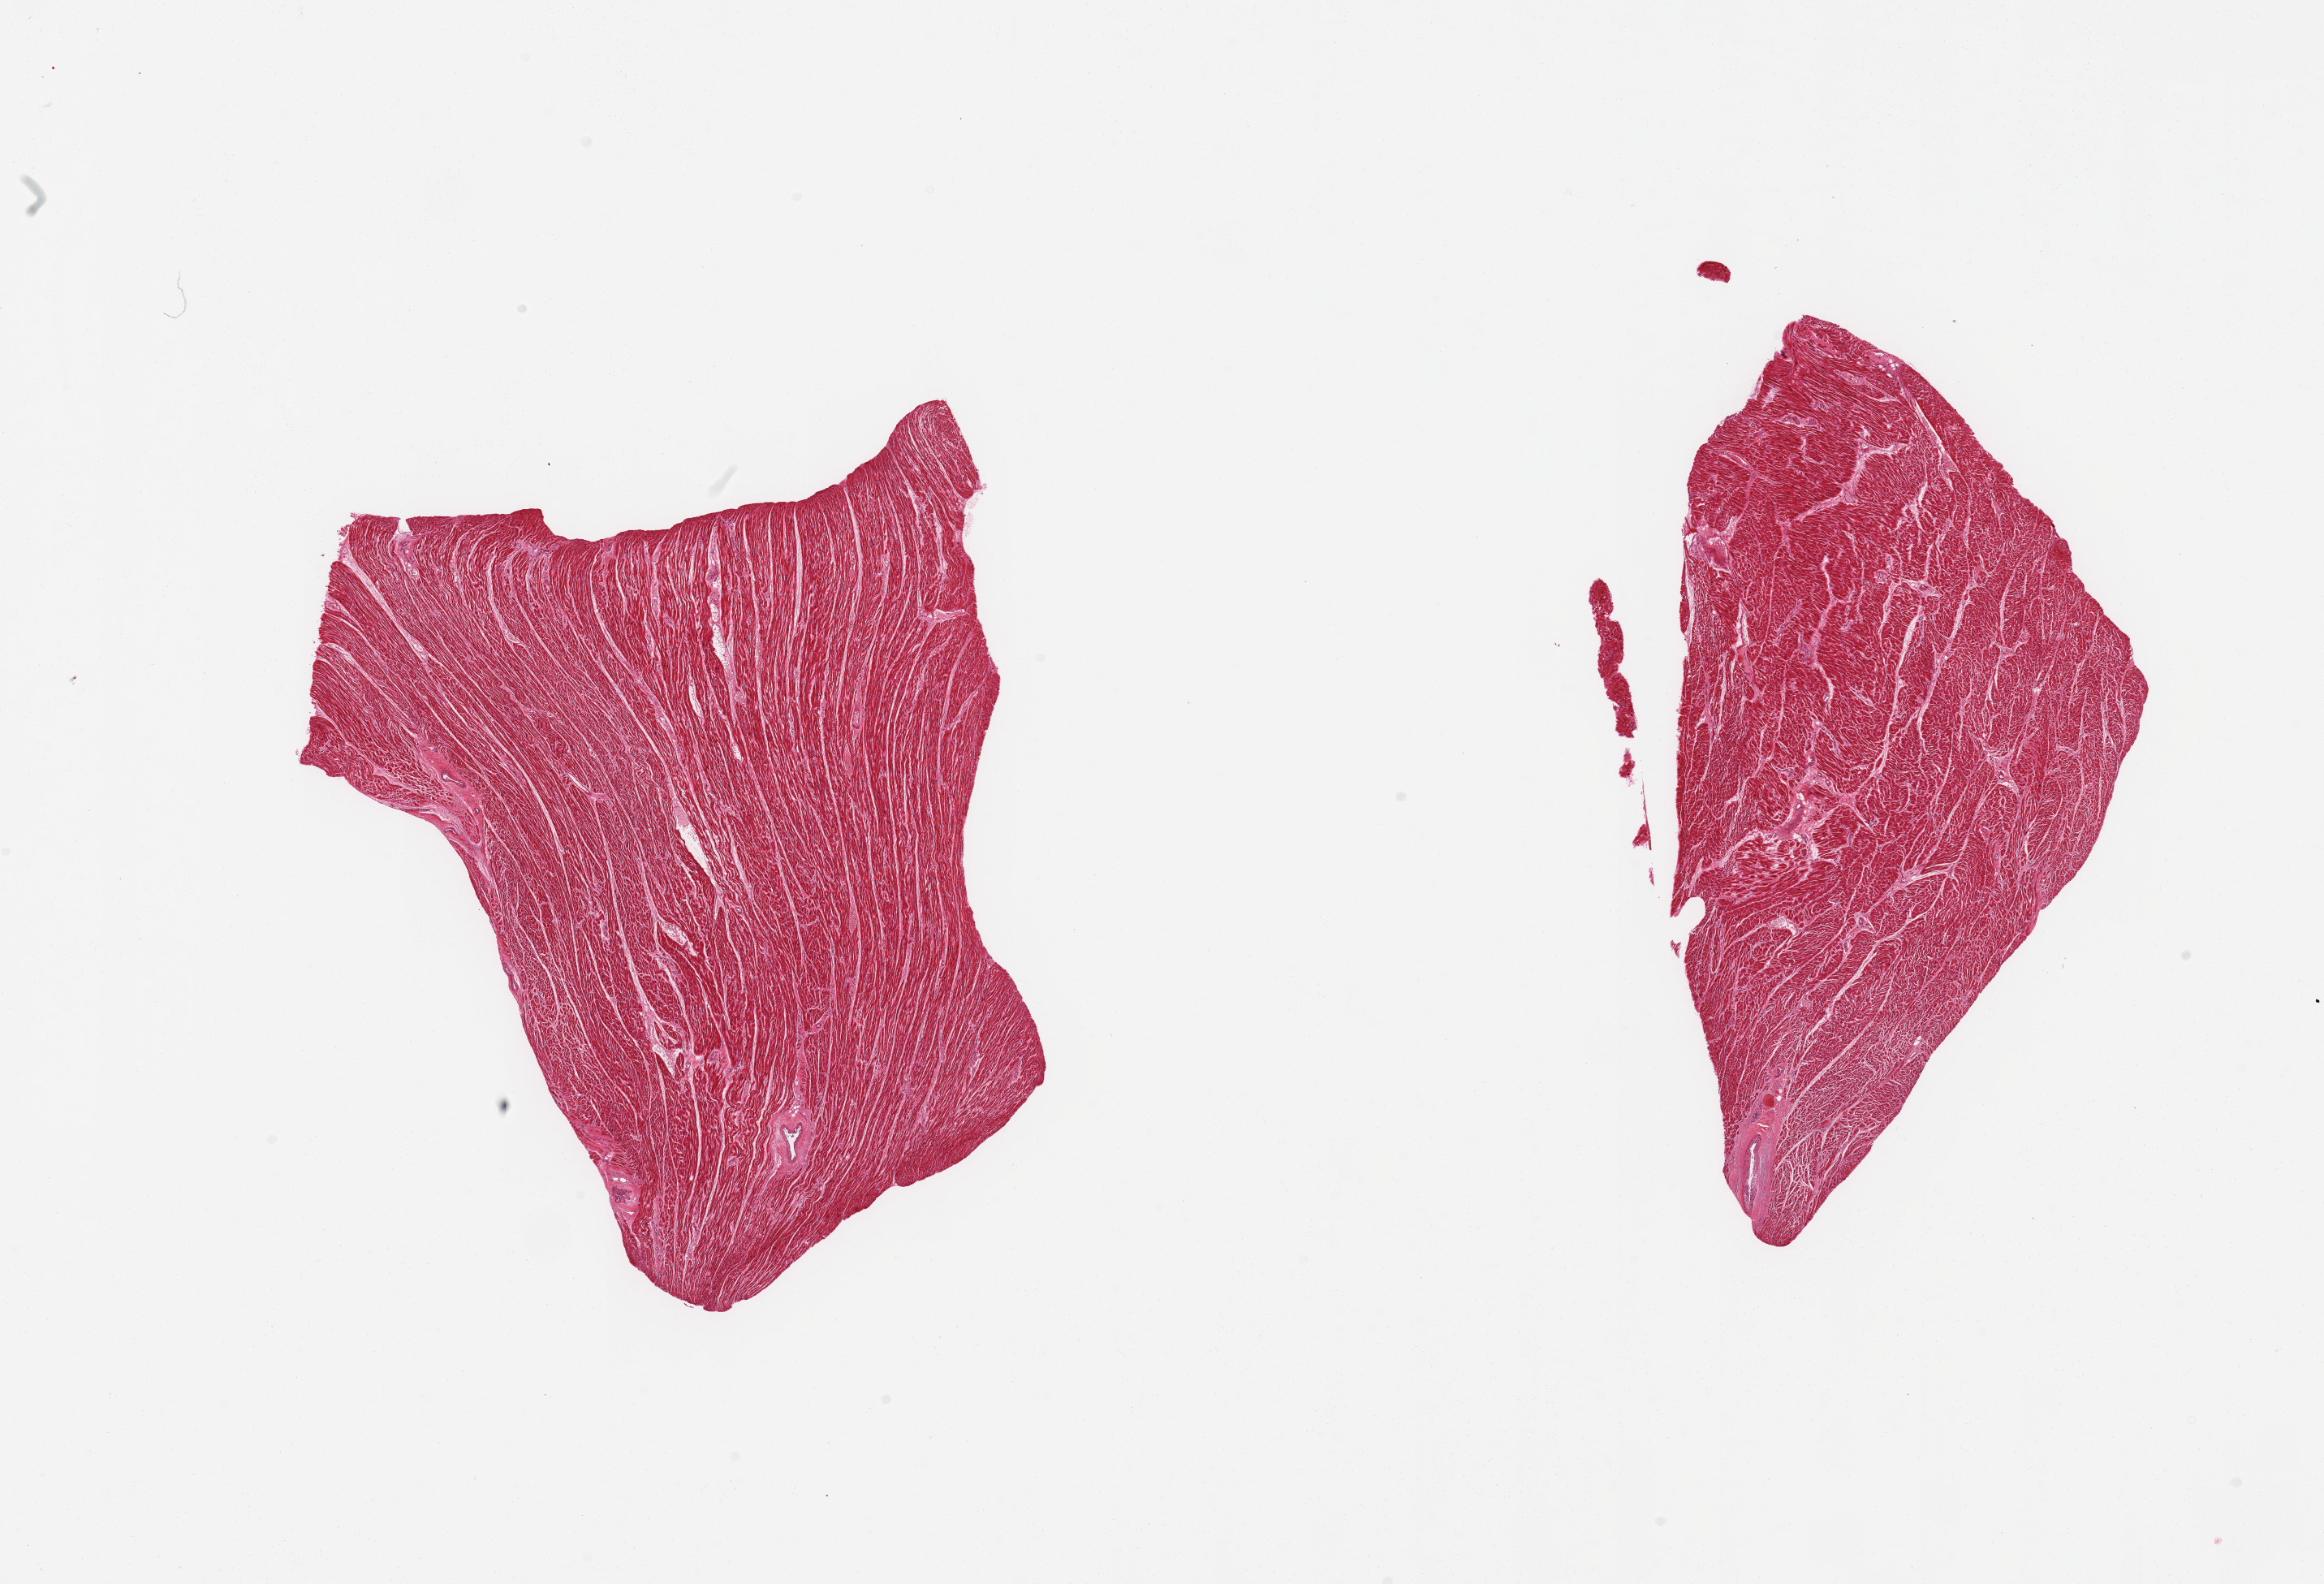
Digitized haematoxylin and eosin-stained section, whole scanned area (about 22.6 x 15.4 mm, from a 20x scan) shown as a low-resolution overview; PAXgene-fixed paraffin-embedded (PFPE) section; target tissue: heart; tissue donor sample. Donor sex: male.
Reviewer comment on this tissue sample: 2 pieces, mild interstitial fibrosis/chronic ischemic change.